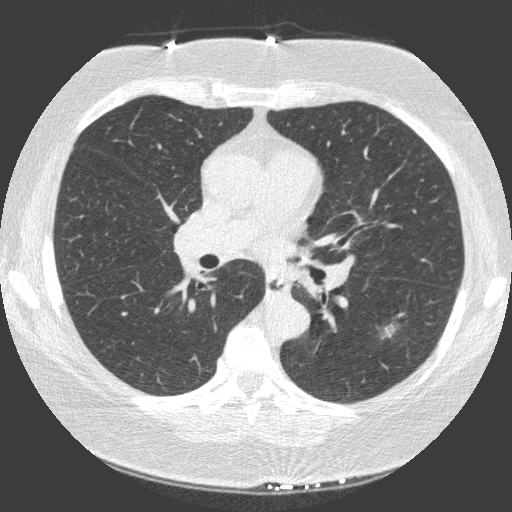
Low-dose screening chest CT, one axial slice; slice 91 of 149 in the series (ordered by position); 120 kVp; lung window (W 1500 / L -600 HU); 1 mm slice thickness; 512 × 512 image matrix, field of view 330 × 330 mm.
Outlined on this slice (expert manual segmentation):
- lesion 1 (tumor, lower lobe of left lung): bounding box <385,325,395,337> (left, top, right, bottom; pixels)